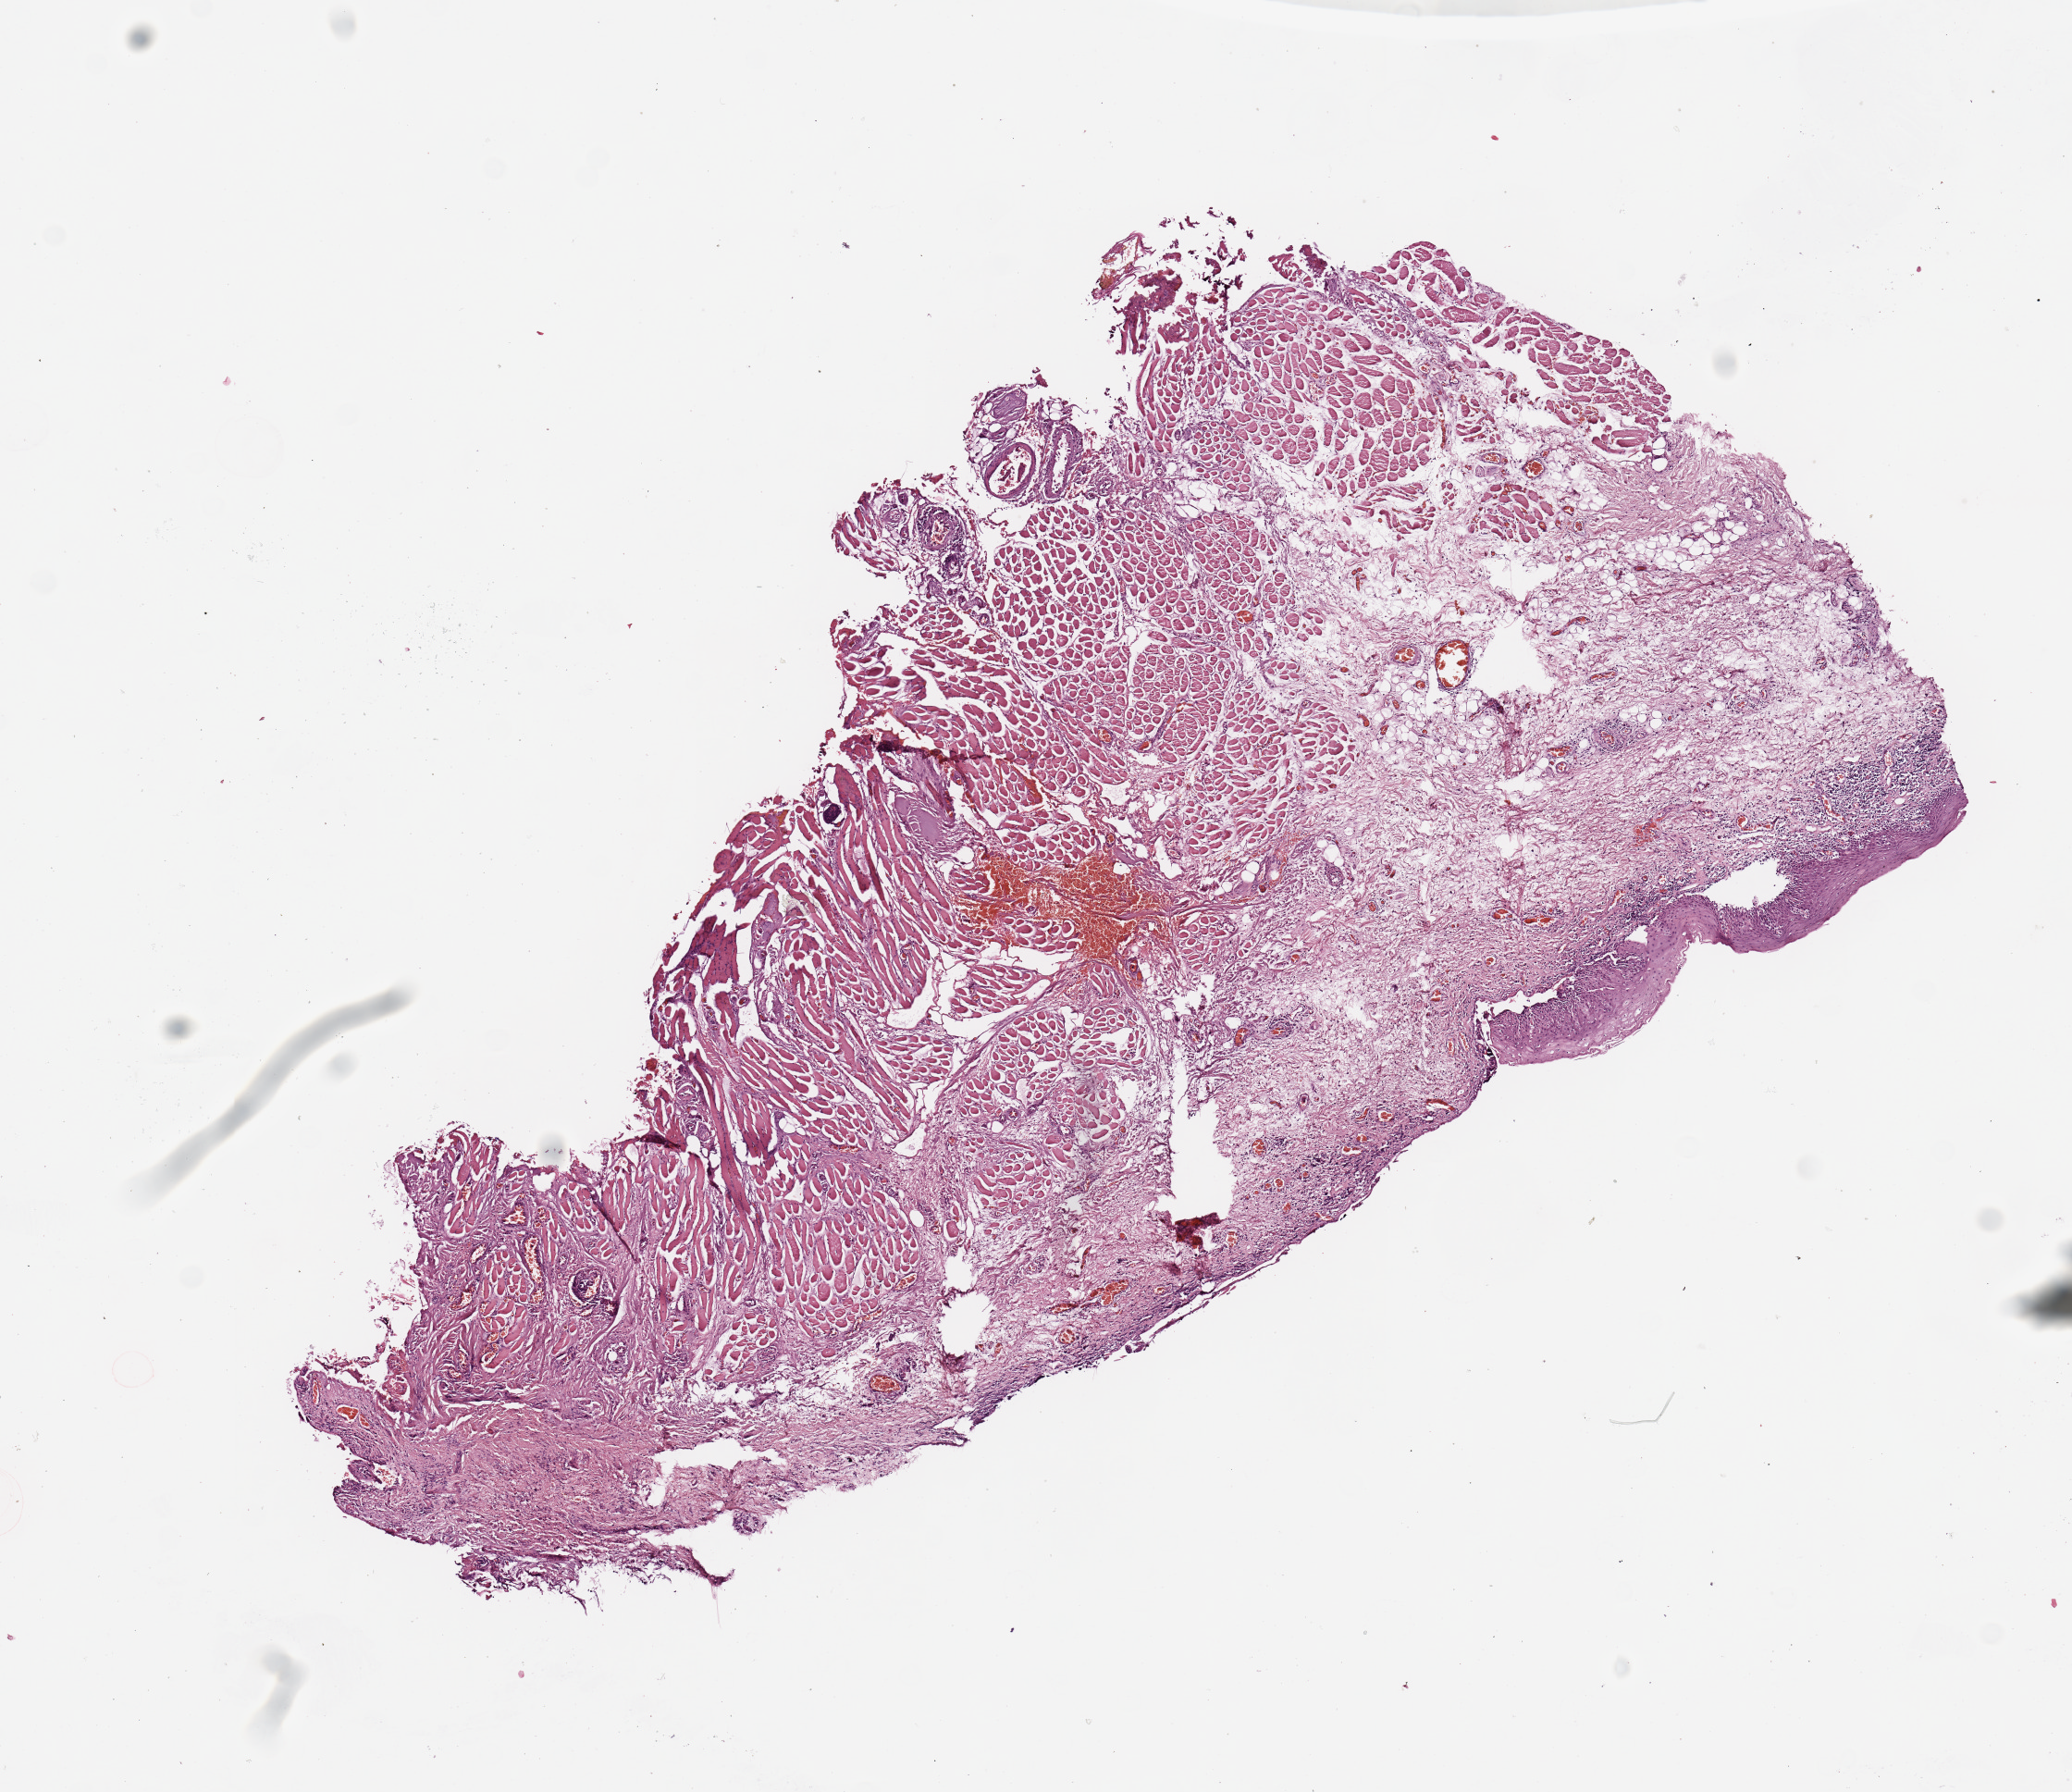
H&E whole-slide image — whole scanned area (about 8.9 x 7.7 mm, acquisition: 20x scan) shown as a low-resolution overview, normal (non-tumour) tissue sample, sampled site: alveolar ridge. Patient: female, age 53 years.
This section: normal (non-tumour) tissue from the same patient. Patient diagnosis: Squamous cell carcinoma, NOS (gum, NOS).